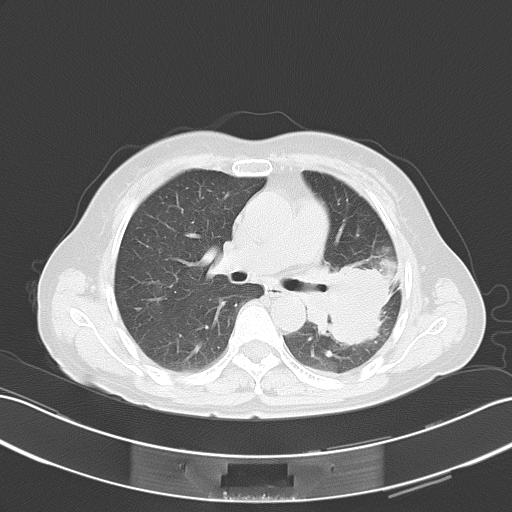
Chest CT, one axial slice. Slice 30 of 51 in the series (ordered by position). 120 kVp. Lung window (W 1500 / L -600 HU). 5 mm slice thickness. 512 × 512 image matrix, field of view 353 × 353 mm. Patient: female, 54 years. Case-level facts recorded for this patient, not image findings: clinical TNM (as recorded): T3 N1 M0.
Structures marked on this image (bounding box drawn by a radiologist):
- lung tumour (recorded histology: adenocarcinoma): bounding box (x1, y1, x2, y2) in pixels: (326, 257, 387, 350)